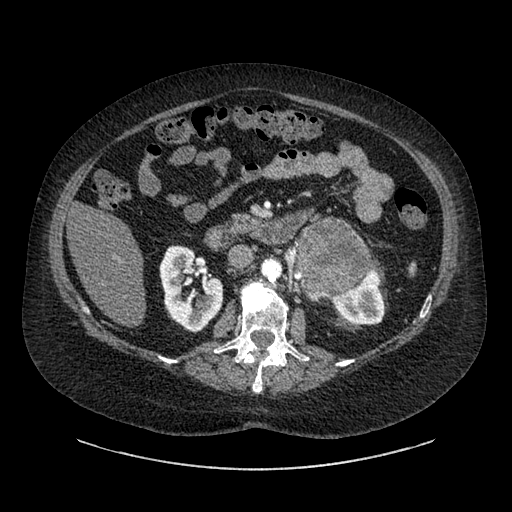
Contrast-enhanced abdominal CT, one axial slice; slice 516 of 769 in the series (ordered by position); reconstruction kernel SOFT; 120 kVp; intravenous contrast given; soft-tissue window (W 400 / L 40 HU); 0.62 mm slice thickness; 512 × 512 image matrix. Female patient, age 61 years. Case-level facts recorded for this patient, not image findings: diagnosis: adrenocortical carcinoma; tumour side: left adrenal; tumour size at pathology: 13 cm; Ki-67 index: 79 %.
Outlined on this slice (semi-automatic segmentation, software-assisted and operator-edited):
- mass: bounding box [x1, y1, x2, y2] px = [298, 221, 371, 294]